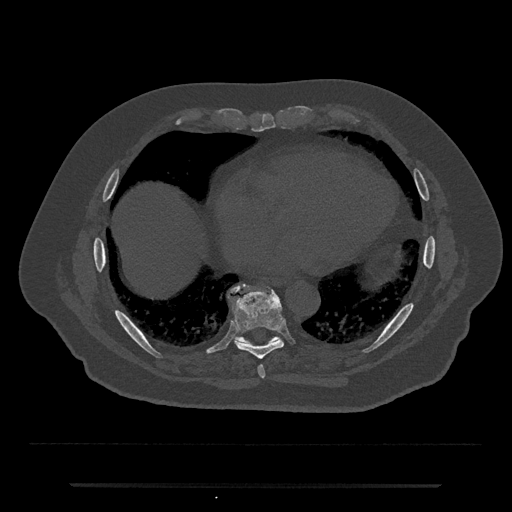
CT including the spine, one axial slice. Slice 797 of 797 in the series (ordered by position). Bone window (W 1800 / L 400 HU). 0.5 mm slice thickness. 512 × 512 image matrix, field of view 434 × 434 mm. Male patient, age 80 years. Case-level facts recorded for this patient, not image findings: primary cancer: prostate; vertebrae with lytic lesions (as recorded): L1, T11.
Structures marked on this image (semi-automatically segmented with operator editing):
- T8 vertebra: bounding box [x1, y1, x2, y2] px = [233, 294, 284, 360]
- T9 vertebra: [229, 285, 280, 347]